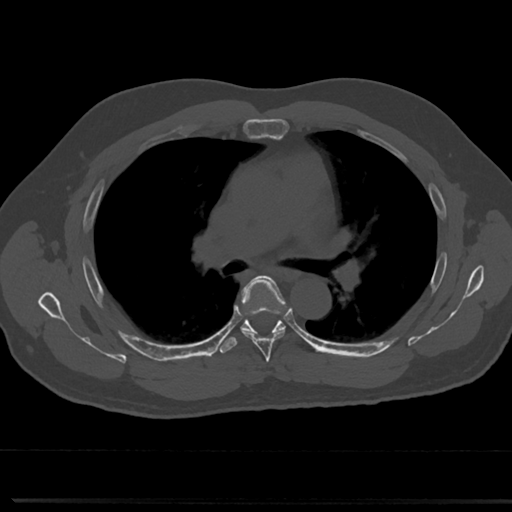
CT including the spine, one axial slice; slice 481 of 817 in the series (ordered by position); bone window (W 1800 / L 400 HU); 0.5 mm slice thickness; 512 × 512 image matrix, field of view 355 × 355 mm. Patient: male, 61 years. From the clinical record (not read from this slice): primary cancer: prostate.
Annotated regions visible in this slice (semi-automatic segmentation, software-assisted and operator-edited):
- T5 vertebra: box from (x=238, y=277) to (x=288, y=358) px
- T6 vertebra: (x=241, y=325)–(x=286, y=334)